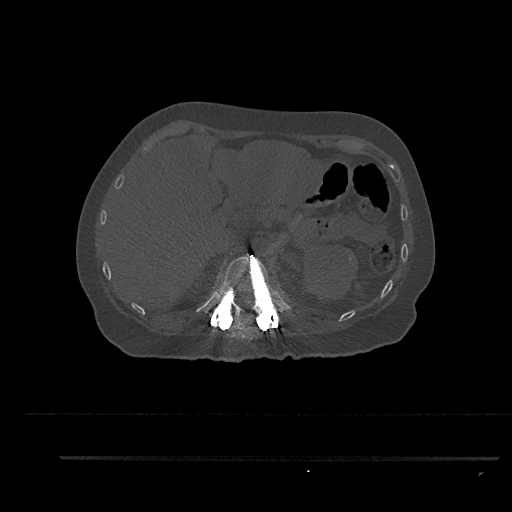
CT including the spine, one axial slice; position 270 of 797 along the scan axis; reconstruction kernel Br40s/3; 120 kVp; bone window (W 1800 / L 400 HU); 0.5 mm slice thickness; 512 × 512 image matrix, field of view 408 × 408 mm. Patient: female, 44 years. Case-level facts recorded for this patient, not image findings: primary cancer: renal; vertebrae with lytic lesions (as recorded): L1.
Outlined on this slice (semi-automatic segmentation, software-assisted and operator-edited):
- T12 vertebra: bounding box <214,253,284,319> (left, top, right, bottom; pixels)